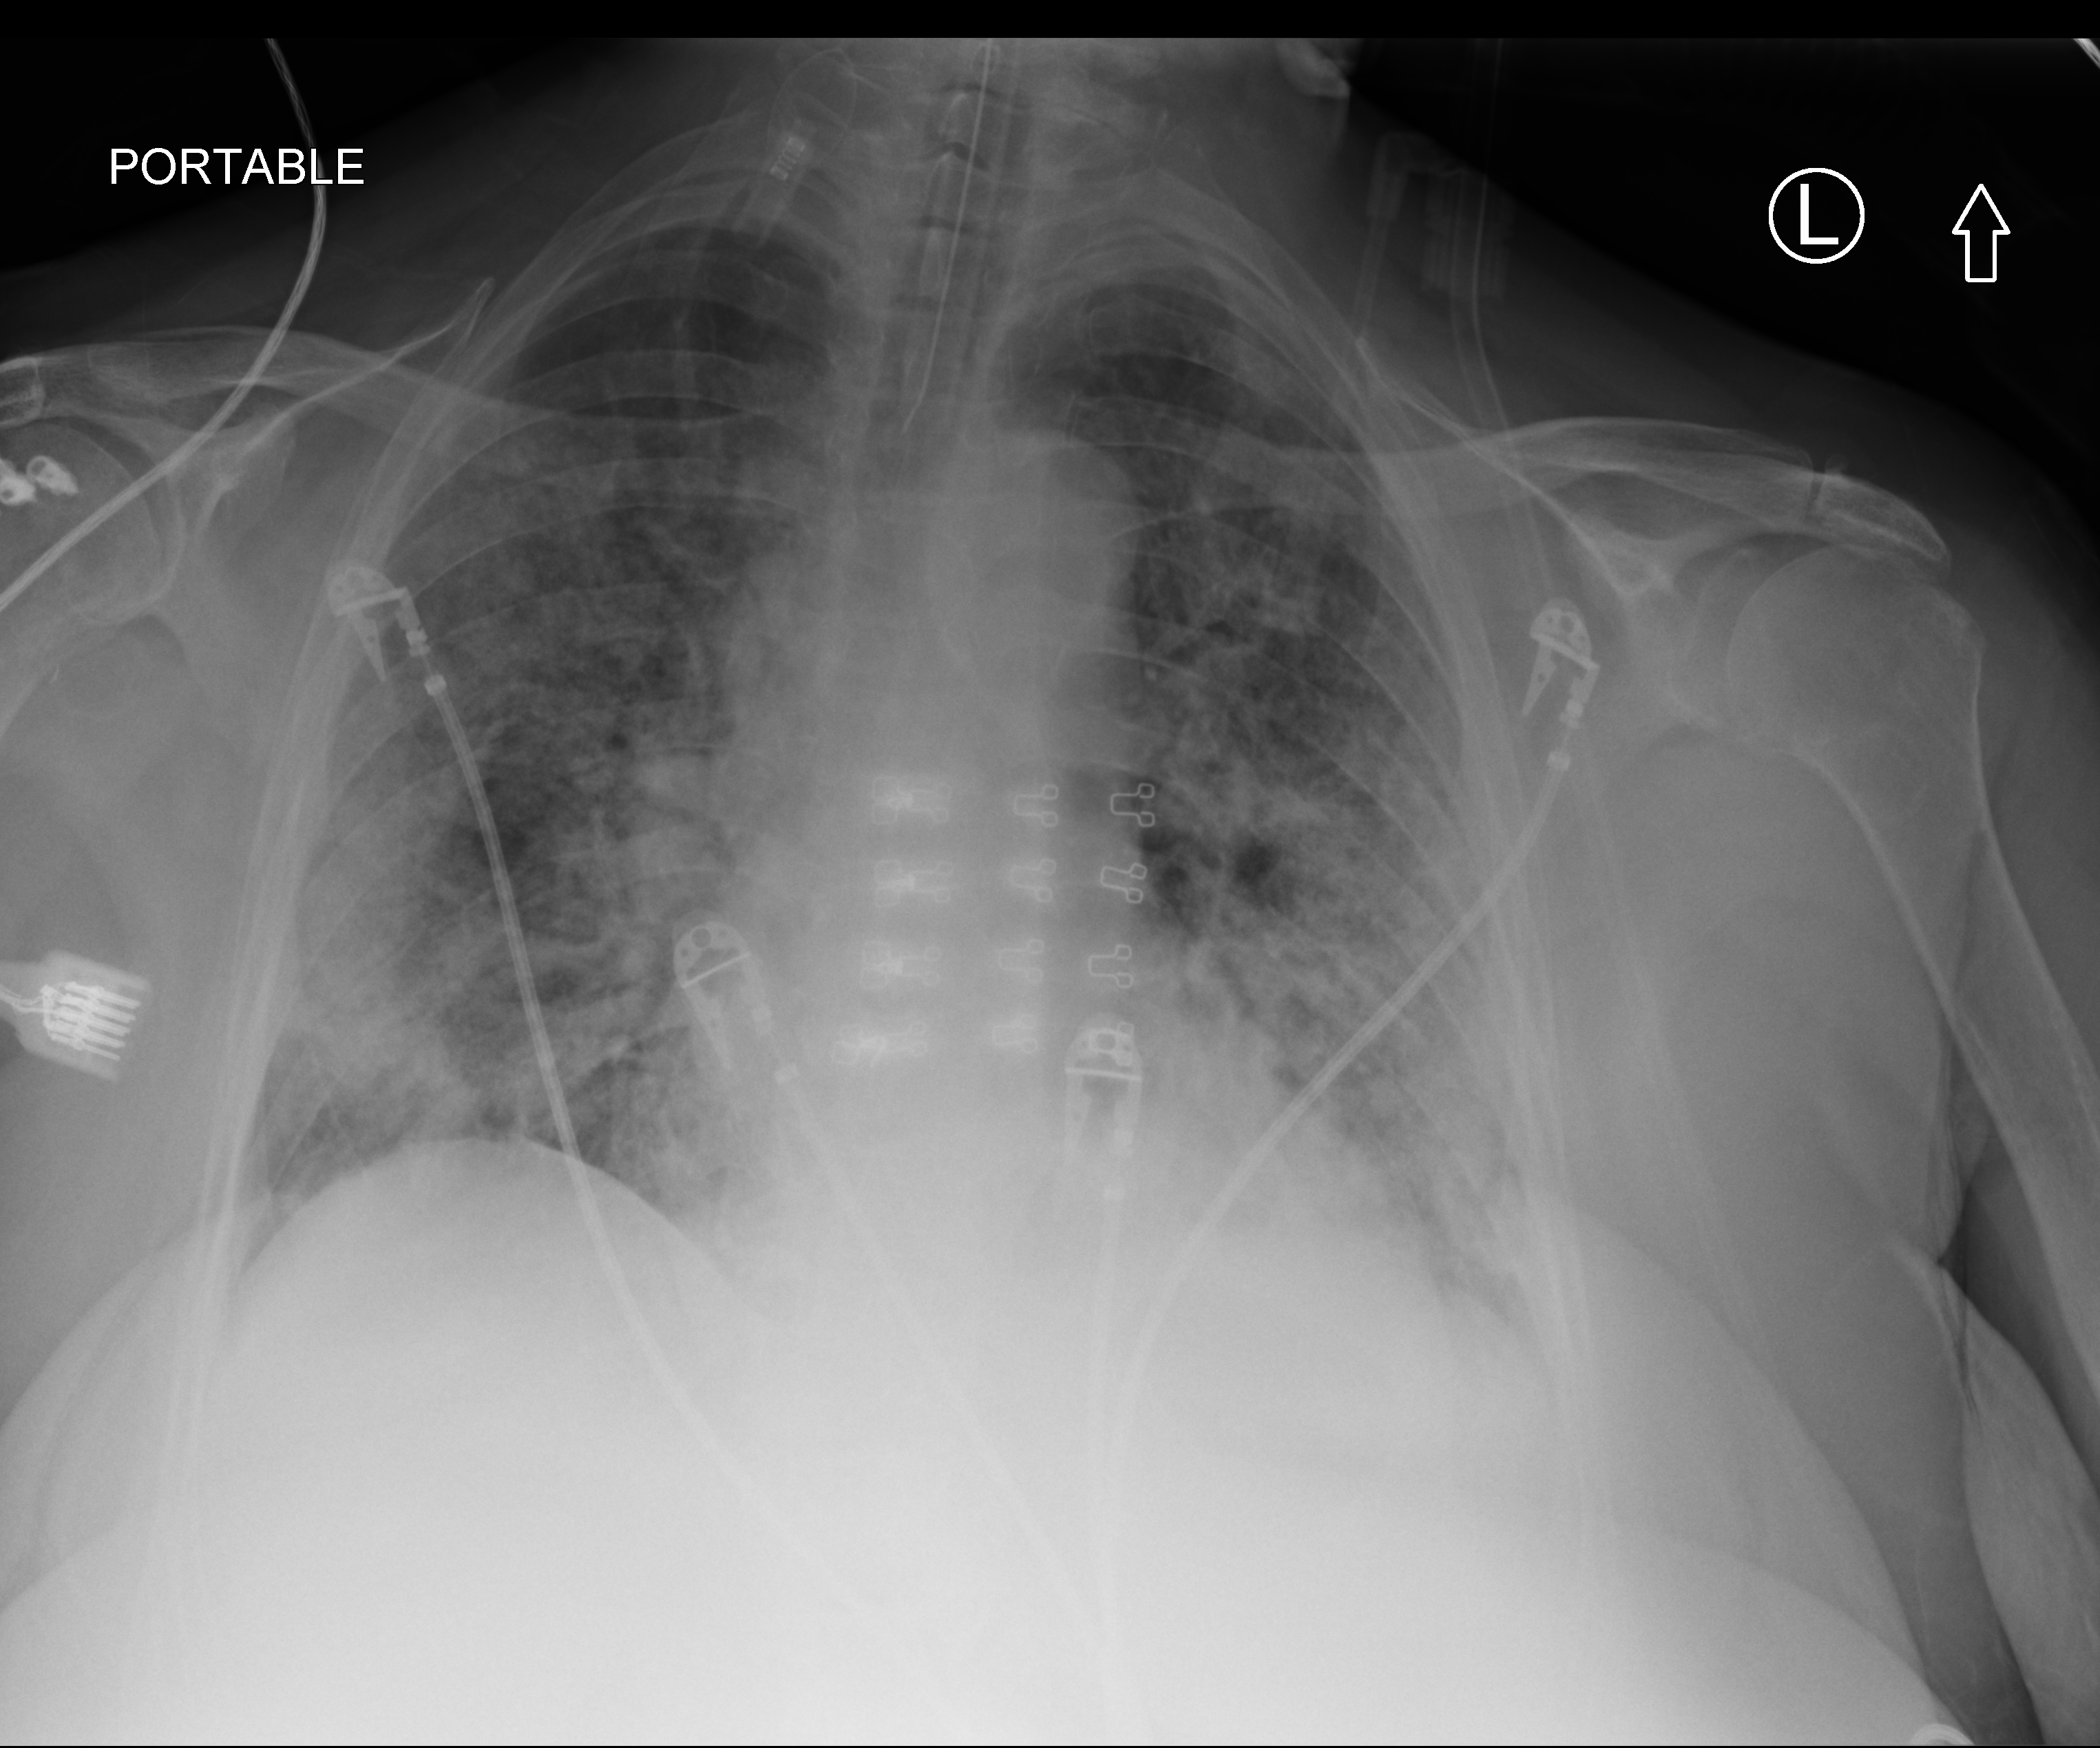
Portable chest radiograph. Patient hospitalised with COVID-19; female, aged 60–74 years.
From the hospital-stay record, not from the radiograph (when in the stay this image was taken is not recorded): length of hospital stay: 19 days; mechanically ventilated during this hospital stay: yes; admitted to intensive care during this hospital stay: yes.